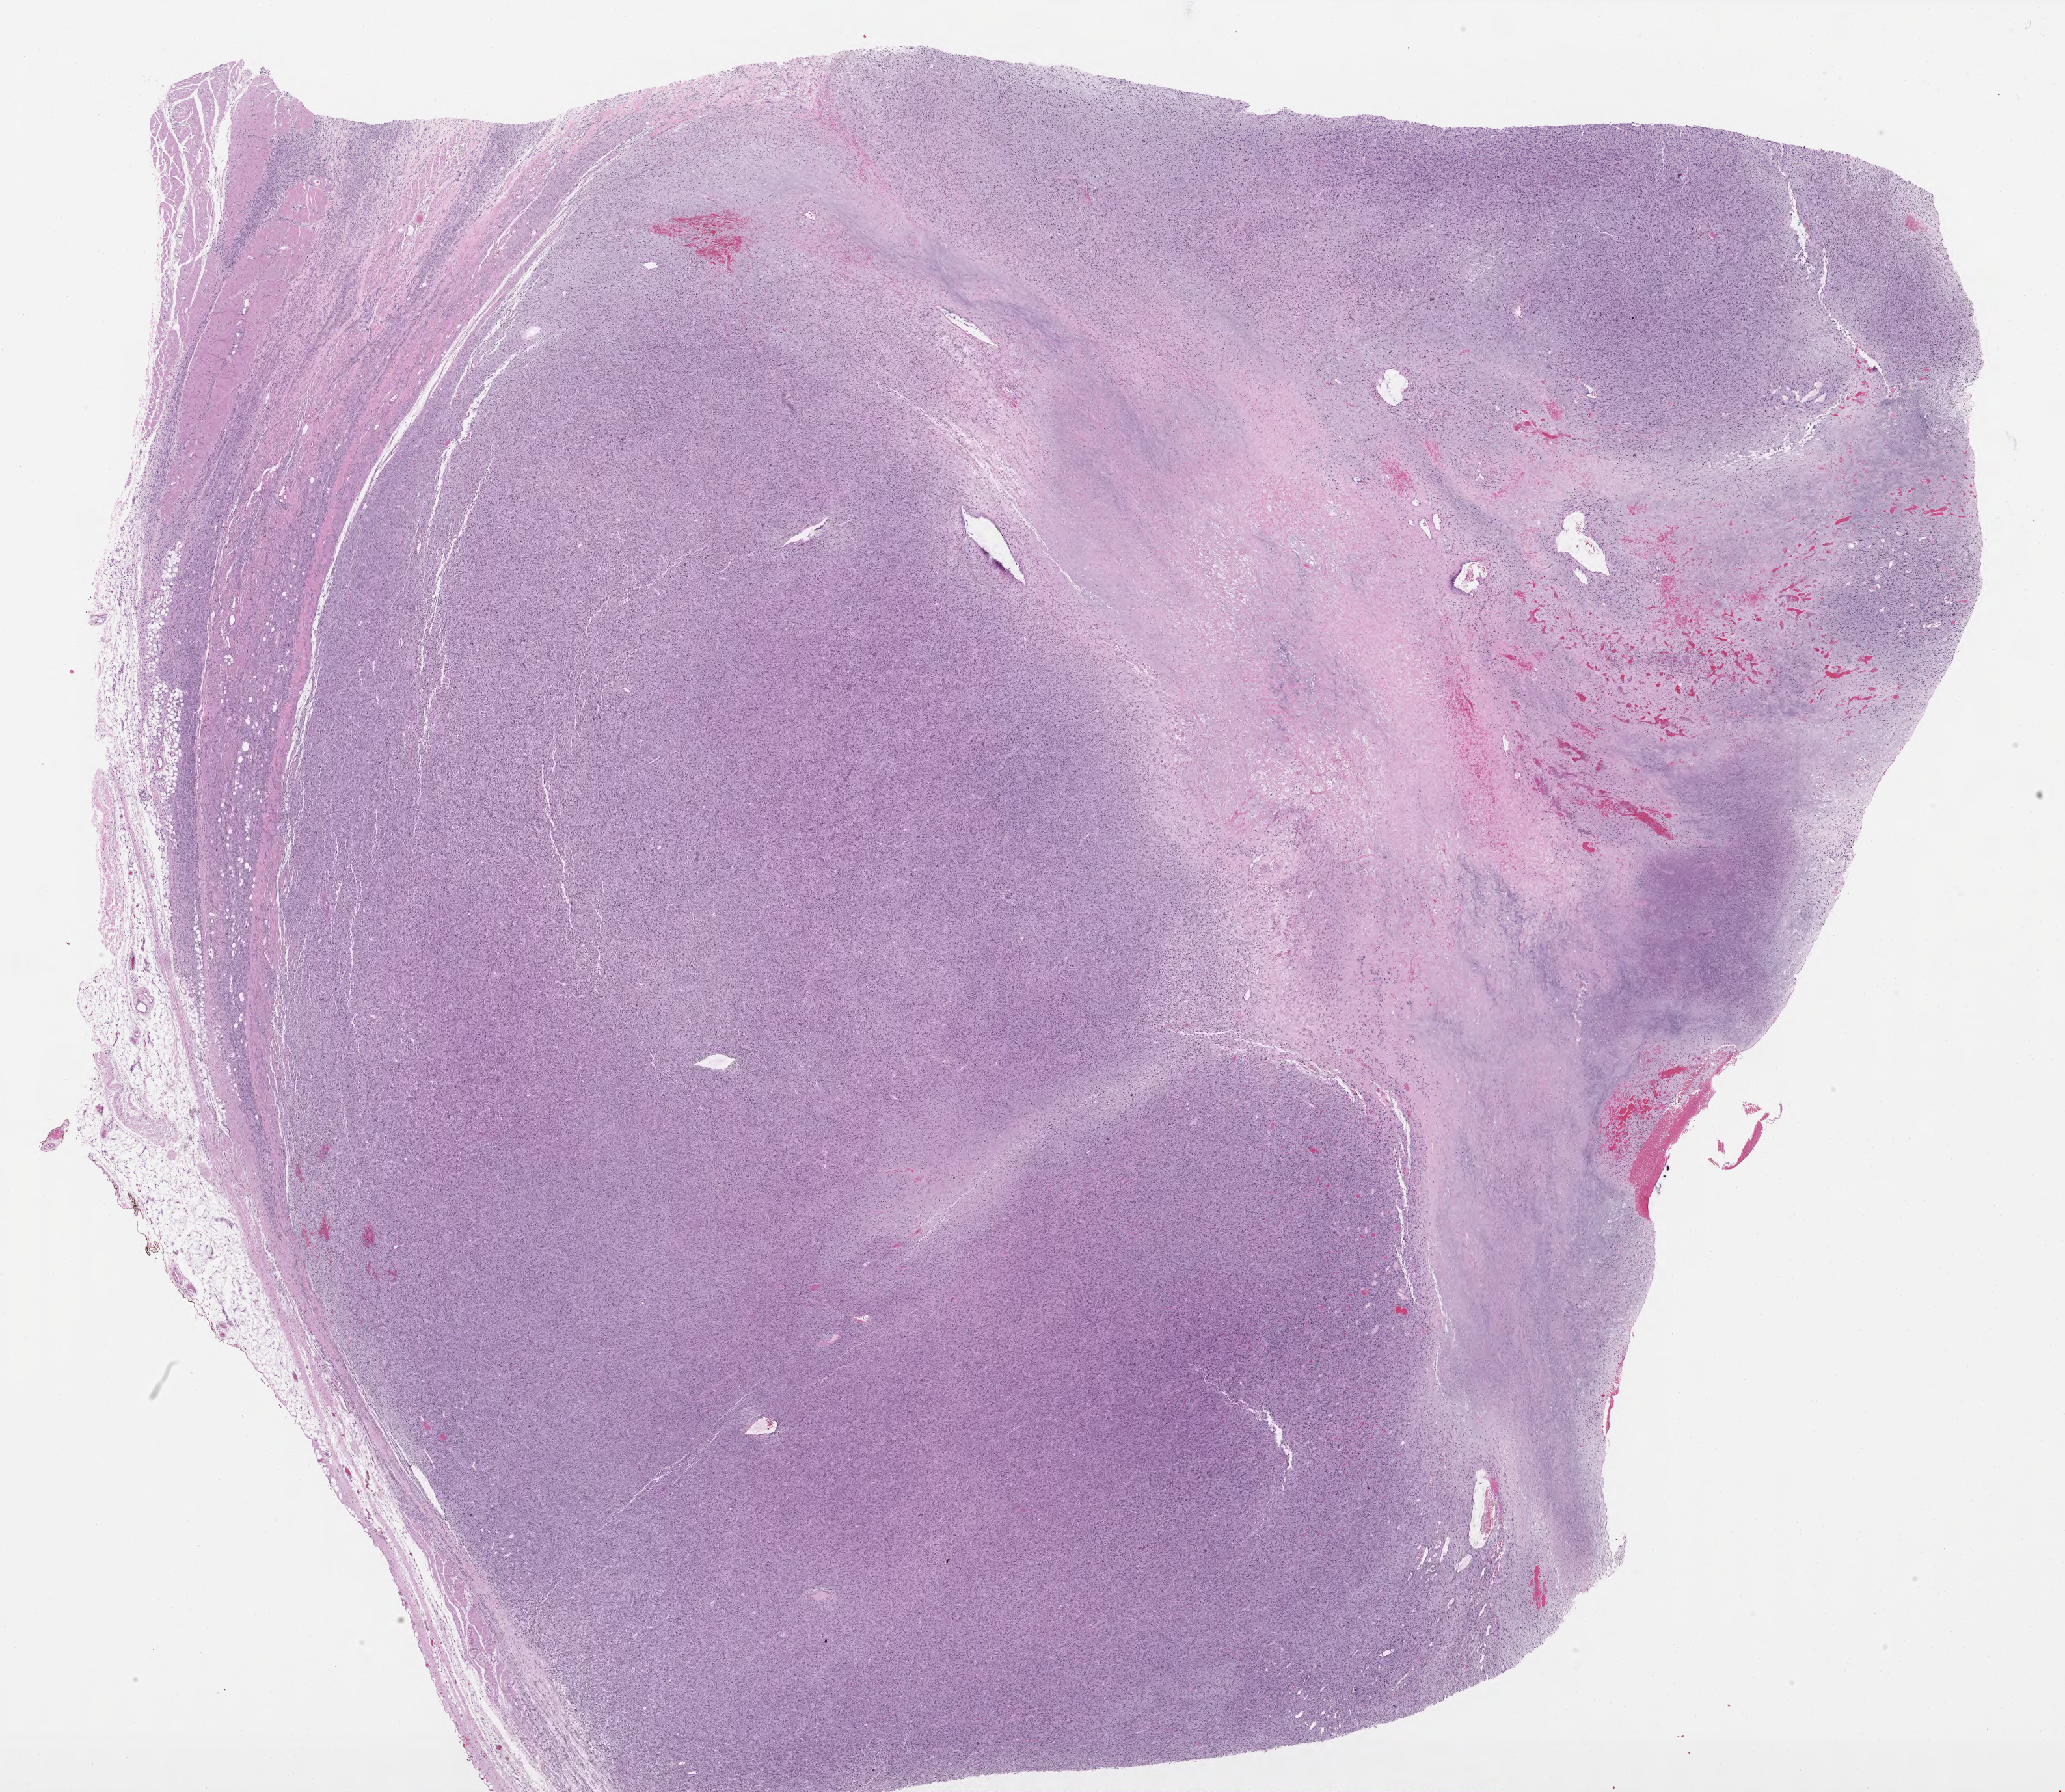
H&E-stained whole-slide image, whole scanned area (about 25.5 x 22.2 mm, from a 40x scan) shown as a low-resolution overview. FFPE section. Connective, subcutaneous and other soft tissues, primary tumour sample. Female, age 78 years at initial diagnosis.
Histologic diagnosis: Undifferentiated sarcoma (connective, subcutaneous and other soft tissues of lower limb and hip).